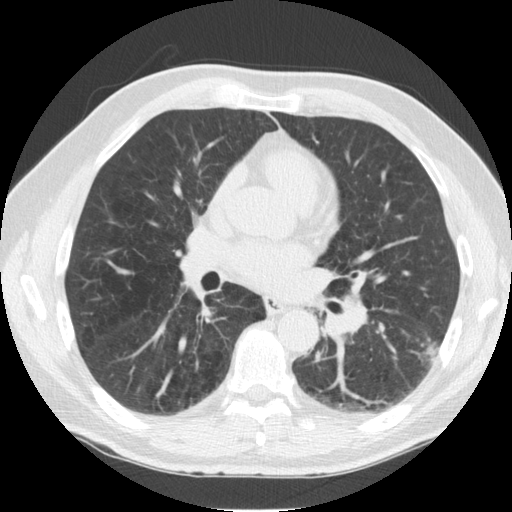
Low-dose screening chest CT, one axial slice; position 58 of 126 along the scan axis; 120 kVp; lung window (W 1500 / L -600 HU); 2.5 mm slice thickness; 512 × 512 image matrix, field of view 344 × 344 mm.
Structures marked on this image (expert manual segmentation):
- lesion 1 (tumor, lower lobe of left lung): bounding box [x1, y1, x2, y2] px = [428, 348, 438, 360]